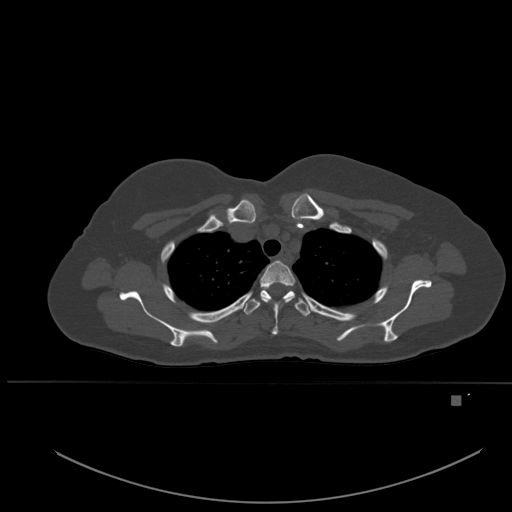
CT including the spine, one axial slice; position 400 of 651 along the scan axis; bone window (W 1800 / L 400 HU); 1.5 mm slice thickness; 512 × 512 image matrix, field of view 443 × 443 mm. Patient: female, 49 years. Case-level facts recorded for this patient, not image findings: primary cancer: breast; vertebrae with lytic lesions (as recorded): L3, T12, L4.
Outlined on this slice (semi-automatically segmented with operator editing):
- T2 vertebra: bounding box <260,260,295,335> (left, top, right, bottom; pixels)
- T3 vertebra: <243,288,311,317>